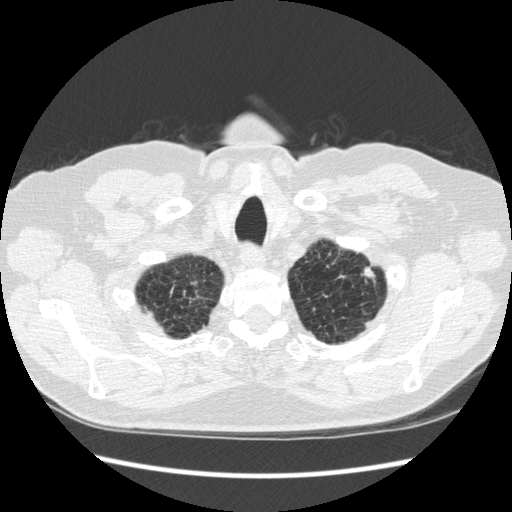
Low-dose screening chest CT, one axial slice. Slice 246 of 267 in the series (ordered by position). Reconstruction kernel STANDARD. Lung window (W 1500 / L -600 HU). 512 × 512 image matrix.
Structures marked on this image (manually delineated by an expert):
- lesion 1 (tumor, upper lobe of left lung): bounding box [x1, y1, x2, y2] px = [364, 267, 375, 277]